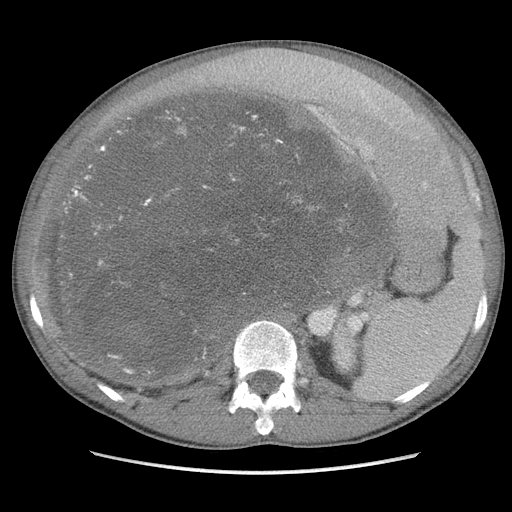
Contrast-enhanced abdominal CT, one axial slice; slice 66 of 115 in the series (ordered by position); soft-tissue window (W 400 / L 40 HU); 512 × 512 image matrix, field of view 360 × 360 mm. Male patient. Case-level facts recorded for this patient, not image findings: diagnosis: adrenocortical carcinoma; tumour side: right adrenal; Ki-67 index: 13 %; stage (as recorded): 3.
Annotated regions visible in this slice (semi-automatic segmentation, software-assisted and operator-edited):
- mass: bounding box <49,97,388,380> (left, top, right, bottom; pixels)